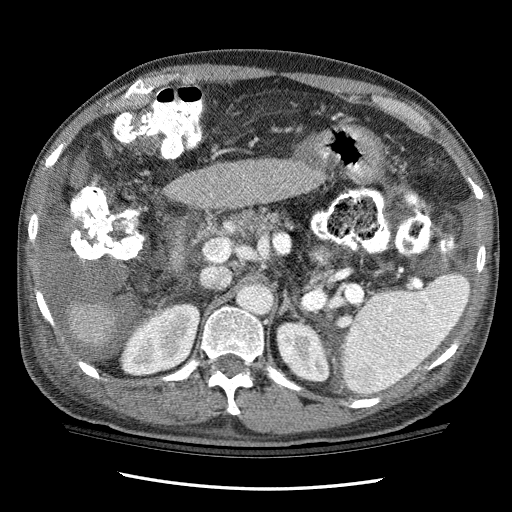
Contrast-enhanced abdominal CT (liver protocol), one axial slice; slice 56 of 114 in the series (ordered by position); 120 kVp; one of 3 acquisitions stored at this slice position; soft-tissue window (W 400 / L 40 HU); 512 × 512 image matrix, field of view 360 × 360 mm. Case-level facts recorded for this patient, not image findings: diagnosis: hepatocellular carcinoma (patient treated with transarterial chemoembolisation; whether this scan precedes or follows treatment is not stated here); TNM stage (as recorded): Stage-I; Child-Pugh class: C; tumour differentiation: well differentiated; tumour nodularity: uninodular.
Annotated regions visible in this slice (semi-automatically segmented with operator editing):
- liver parenchyma outside the tumour (the mass and vessels are separate outlines, so this box may not span the whole liver): box from (x=70, y=157) to (x=321, y=344) px